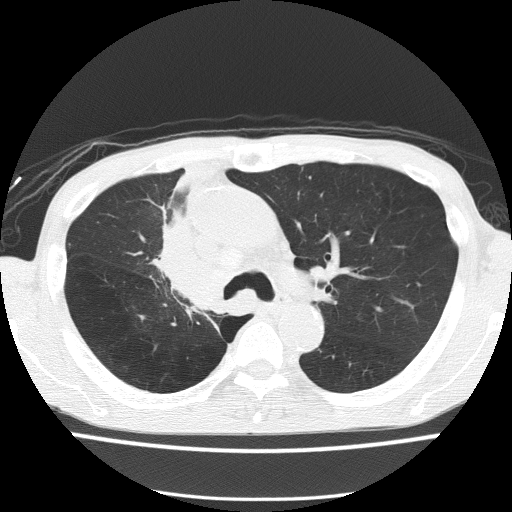
Chest CT (low-dose screening protocol), one axial image, baseline screening round, lung window (W 1500 / L -600 HU), 2 mm slice thickness, slice 51 of 150 in the series. Male participant, aged 59 years at enrolment.
- Expert-annotated lung lesion, bounding box (x1, y1, x2, y2) in pixels: (139, 231, 234, 322).
- The screening reader recorded 5 non-calcified nodules or masses ≥4 mm on this exam; which of them this box marks is not recorded.
- Official screen result: positive, change unspecified: nodule(s) >= 4 mm or enlarging nodule(s), mass(es), or other non-specific abnormalities suspicious for lung cancer.
- Later outcome: lung cancer diagnosed 72 days after this screen — squamous cell carcinoma, NOS, right upper lobe, moderately differentiated (G2), stage IV (AJCC 6th edition).